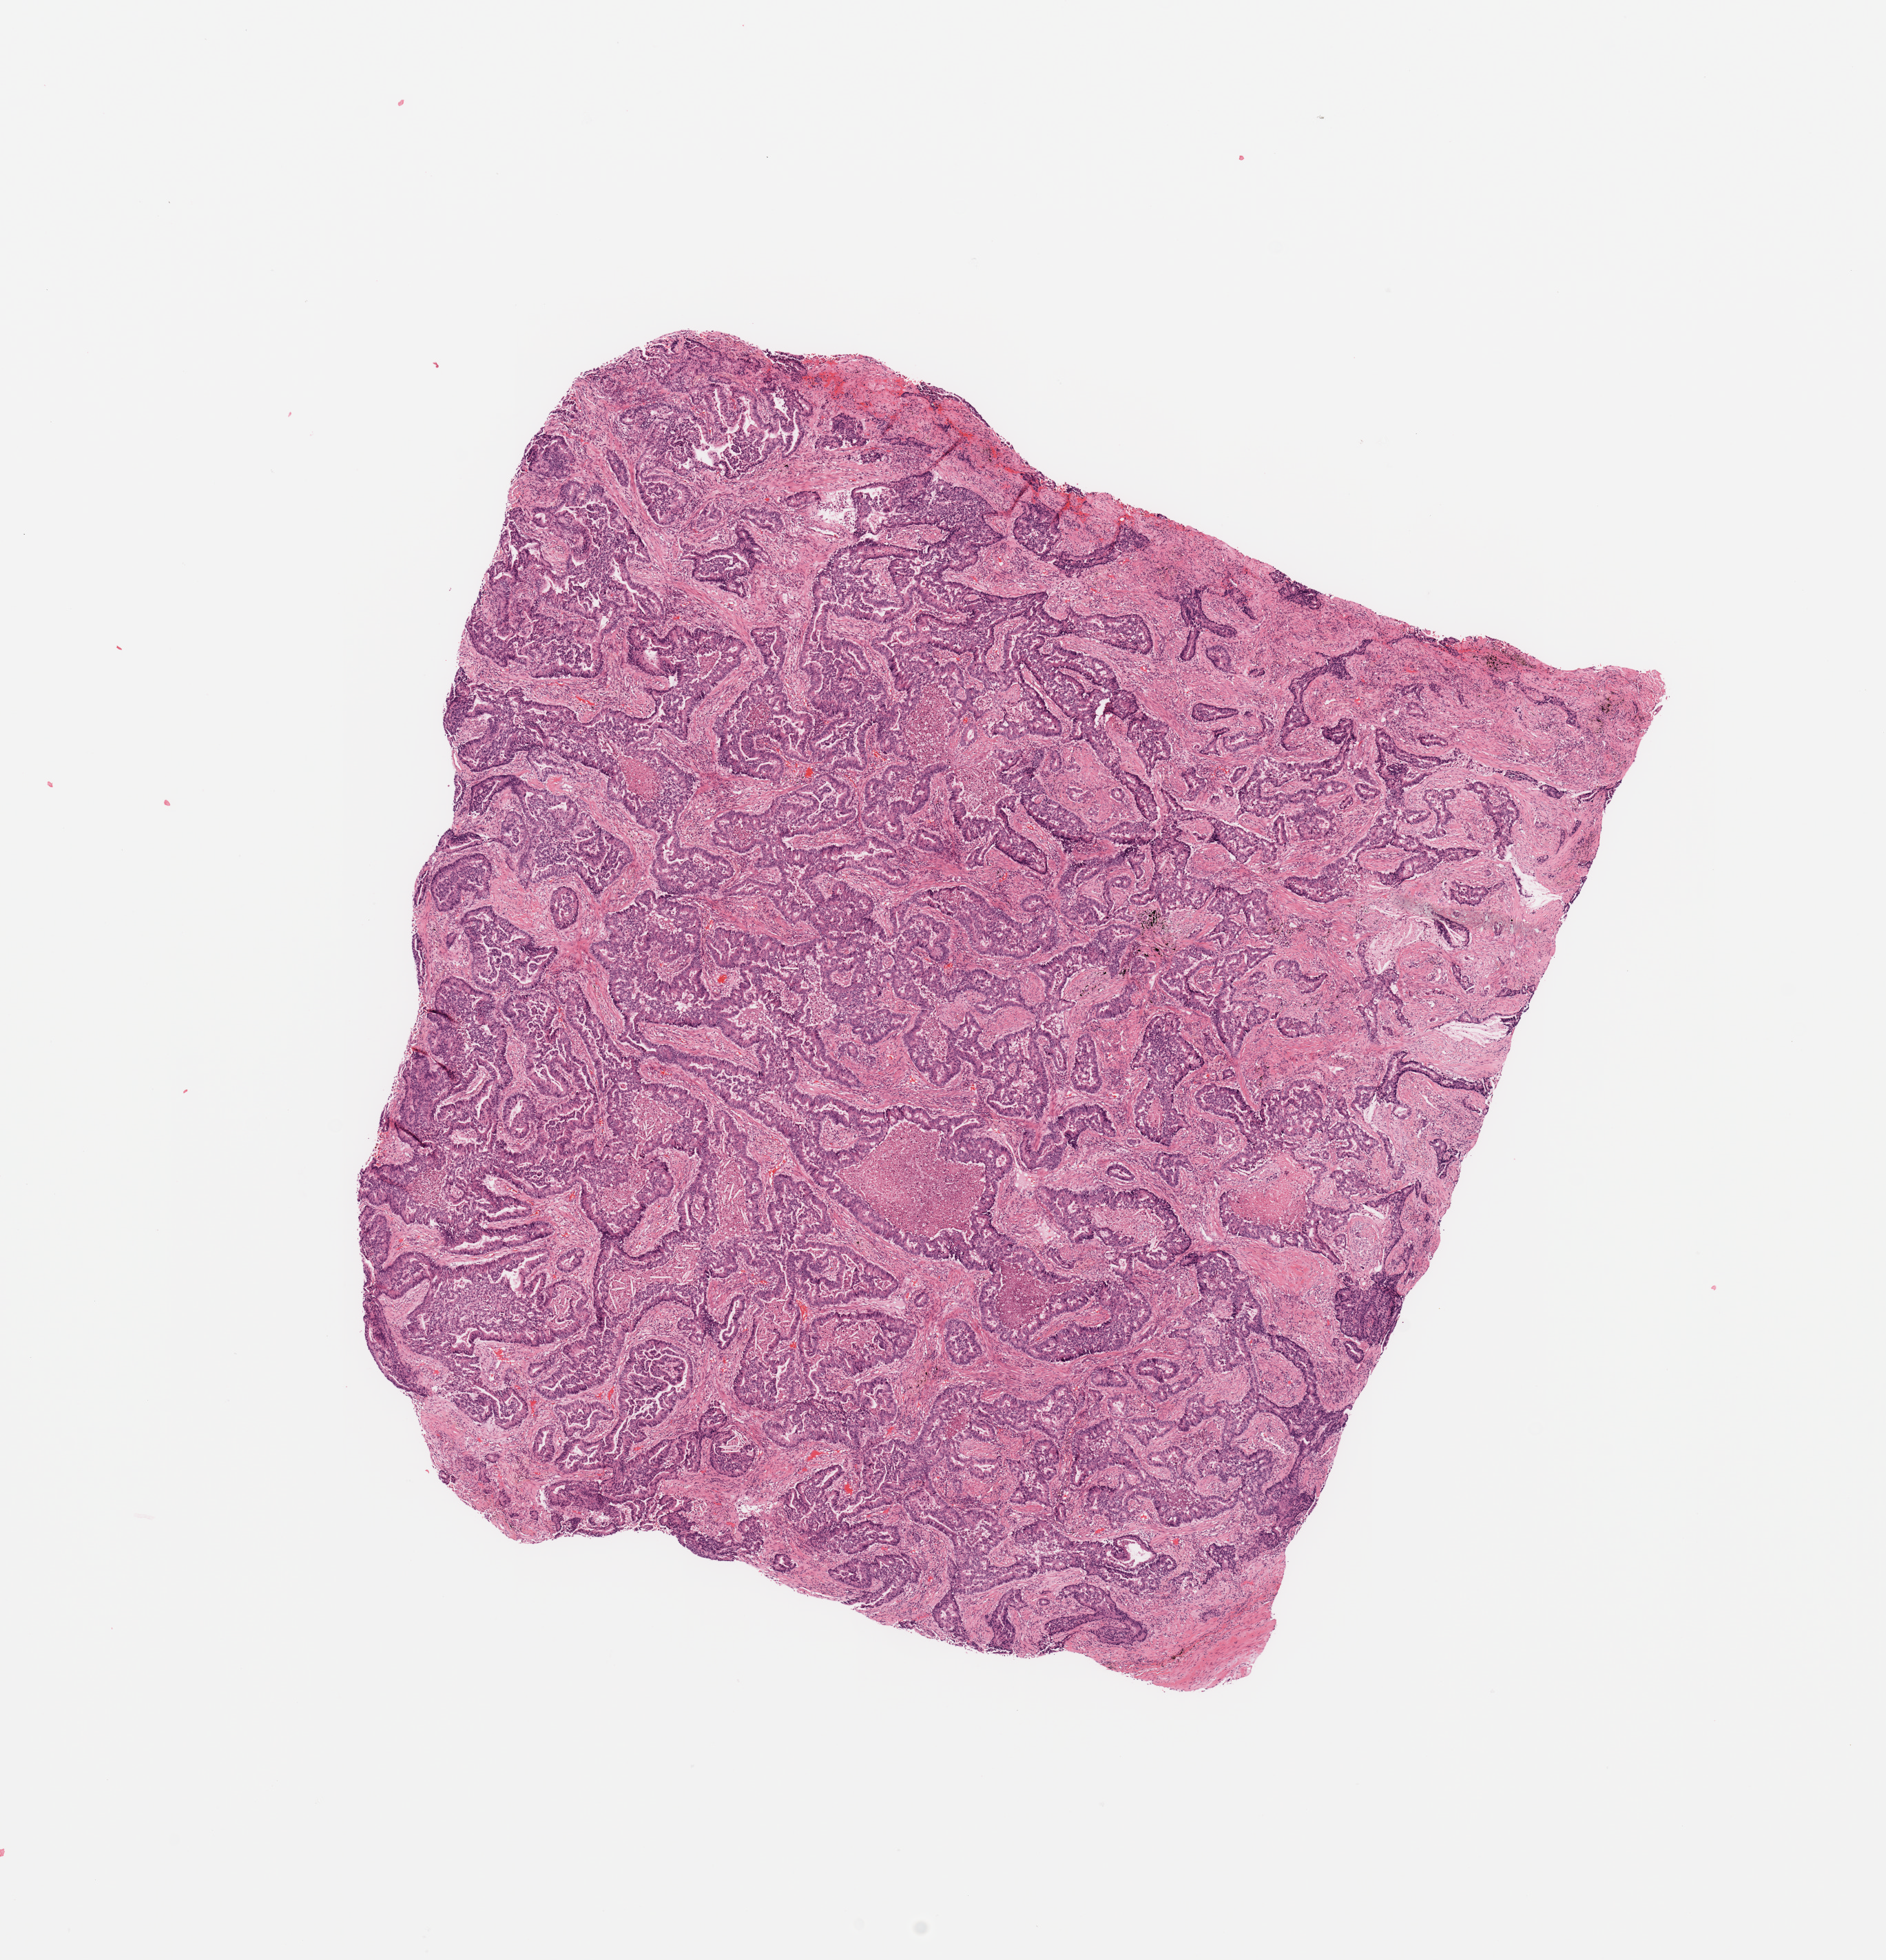
H&E whole-slide image, a low-resolution overview of the entire scanned area, about 10.8 x 11.3 mm; lung, tumour tissue. 59-year-old female patient.
Diagnosis: Adenocarcinoma, NOS.